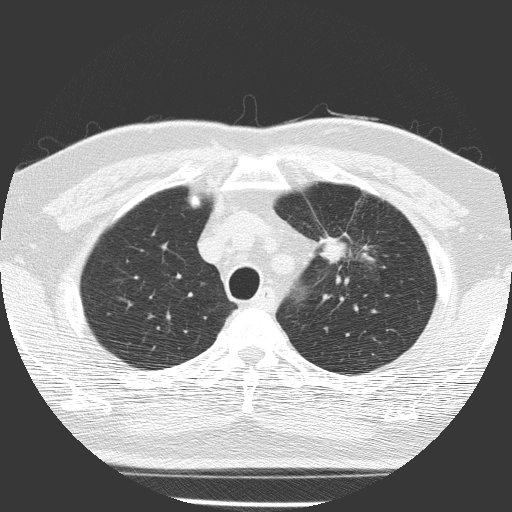
Low-dose screening chest CT, one axial slice. Slice 121 of 156 in the series (ordered by position). Lung window (W 1500 / L -600 HU). 512 × 512 image matrix, field of view 309 × 309 mm.
Structures marked on this image (expert manual segmentation):
- lesion 1 (tumor, upper lobe of left lung): bounding box <322,239,347,263> (left, top, right, bottom; pixels)